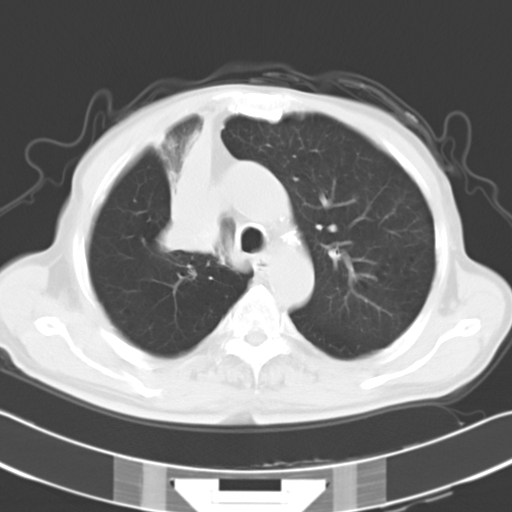
Chest CT, one axial slice; reconstruction kernel B40f; 120 kVp; lung window (W 1500 / L -600 HU); 512 × 512 image matrix. Patient: male, 73 years. Case-level facts recorded for this patient, not image findings: clinical TNM (as recorded): T2a N1 M0.
Outlined on this slice (rectangle marked by the reading radiologist):
- lung tumour (recorded histology: squamous cell carcinoma): bounding box (x1, y1, x2, y2) in pixels: (166, 114, 231, 266)